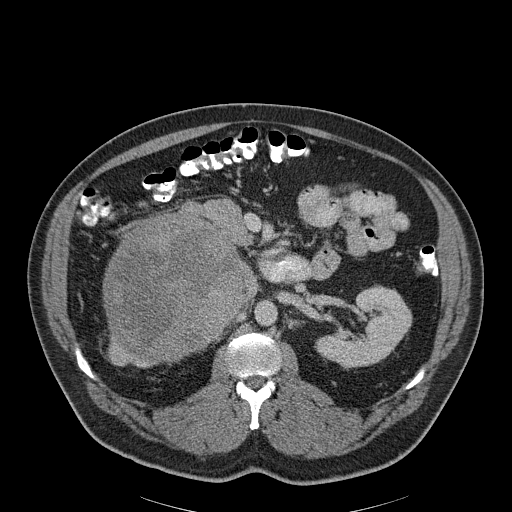
Contrast-enhanced abdominal CT, one axial slice; slice 117 of 186 in the series (ordered by position); soft-tissue window (W 400 / L 40 HU); 3 mm slice thickness; 512 × 512 image matrix, field of view 464 × 464 mm. Patient: male, 56 years. From the clinical record (not read from this slice): diagnosis: adrenocortical carcinoma; tumour side: right adrenal; tumour size at pathology: 18 cm; Ki-67 index: 2 %; stage (as recorded): 3.
Outlined on this slice (semi-automatic segmentation, software-assisted and operator-edited):
- mass: box from (x=106, y=217) to (x=241, y=360) px